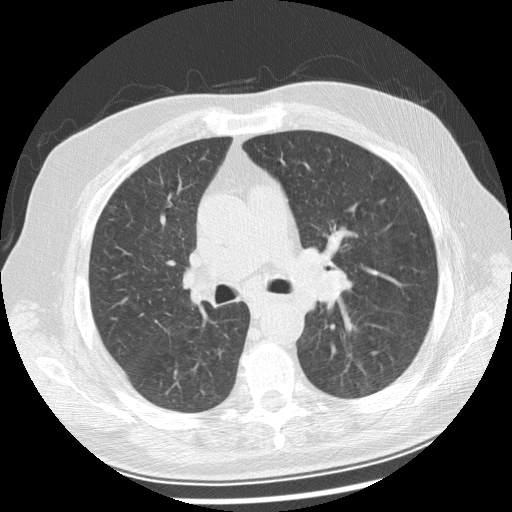
Axial slice from a low-dose chest CT screening exam; first (baseline) screen; lung window (W 1500 / L -600 HU); 2.5 mm slice thickness; standard (soft-tissue) reconstruction kernel (STANDARD); slice 100 of 250 in the series; 512 × 512 image matrix, field of view 360 × 360 mm. Male, age 70 years at enrolment.
Lesion marked by an expert reader, bounding box <280,242,361,307> (left, top, right, bottom; pixels). No non-calcified nodule or mass ≥4 mm was recorded by the screening reader at this exam. Official screen result: positive, change unspecified: nodule(s) >= 4 mm or enlarging nodule(s), mass(es), or other non-specific abnormalities suspicious for lung cancer. Lung cancer was diagnosed 29 days after this screen: squamous cell carcinoma, keratinizing, NOS, left main stem bronchus, moderately differentiated (G2), stage IIIB (AJCC 6th edition), 40 mm at pathology.